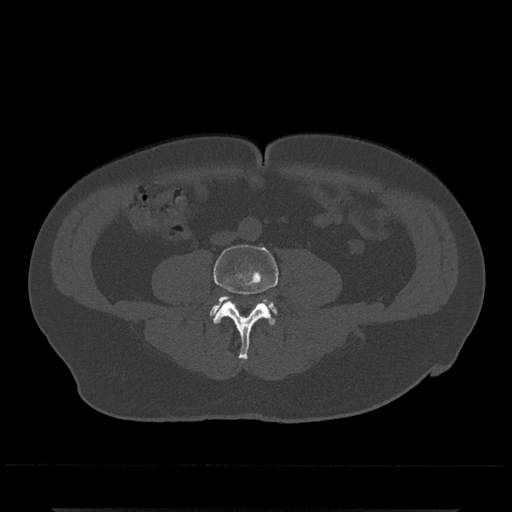
CT including the spine, one axial slice. Position 142 of 797 along the scan axis. Reconstruction kernel Br40s/3. 120 kVp. Bone window (W 1800 / L 400 HU). 0.5 mm slice thickness. 512 × 512 image matrix, field of view 393 × 393 mm. Patient: male, 67 years. From the clinical record (not read from this slice): primary cancer: prostate.
Outlined on this slice (semi-automatic segmentation, software-assisted and operator-edited):
- L4 vertebra: bounding box (x1, y1, x2, y2) in pixels: (213, 244, 278, 360)
- L5 vertebra: (210, 296, 276, 318)